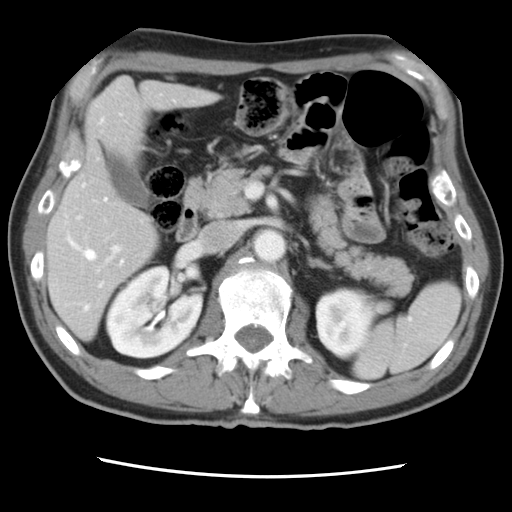
Contrast-enhanced abdominal CT, one axial slice; position 42 of 83 along the scan axis; intravenous contrast given; soft-tissue window (W 400 / L 40 HU); 5 mm slice thickness; 512 × 512 image matrix, field of view 321 × 321 mm. Male patient, age 69 years. From the clinical record (not read from this slice): diagnosis: colorectal cancer liver metastases, imaged before liver resection; multiple liver metastases: yes; largest metastasis: 3.5 cm; chemotherapy before resection: yes.
Outlined on this slice (manually delineated by an expert):
- hepatic veins: box from (x=68, y=119) to (x=124, y=310) px
- liver: (x=49, y=78)–(x=214, y=338)
- planned liver remnant (the part of the liver to remain after resection): (x=49, y=148)–(x=158, y=339)
- portal vein (with intrahepatic branches): (x=76, y=183)–(x=122, y=272)